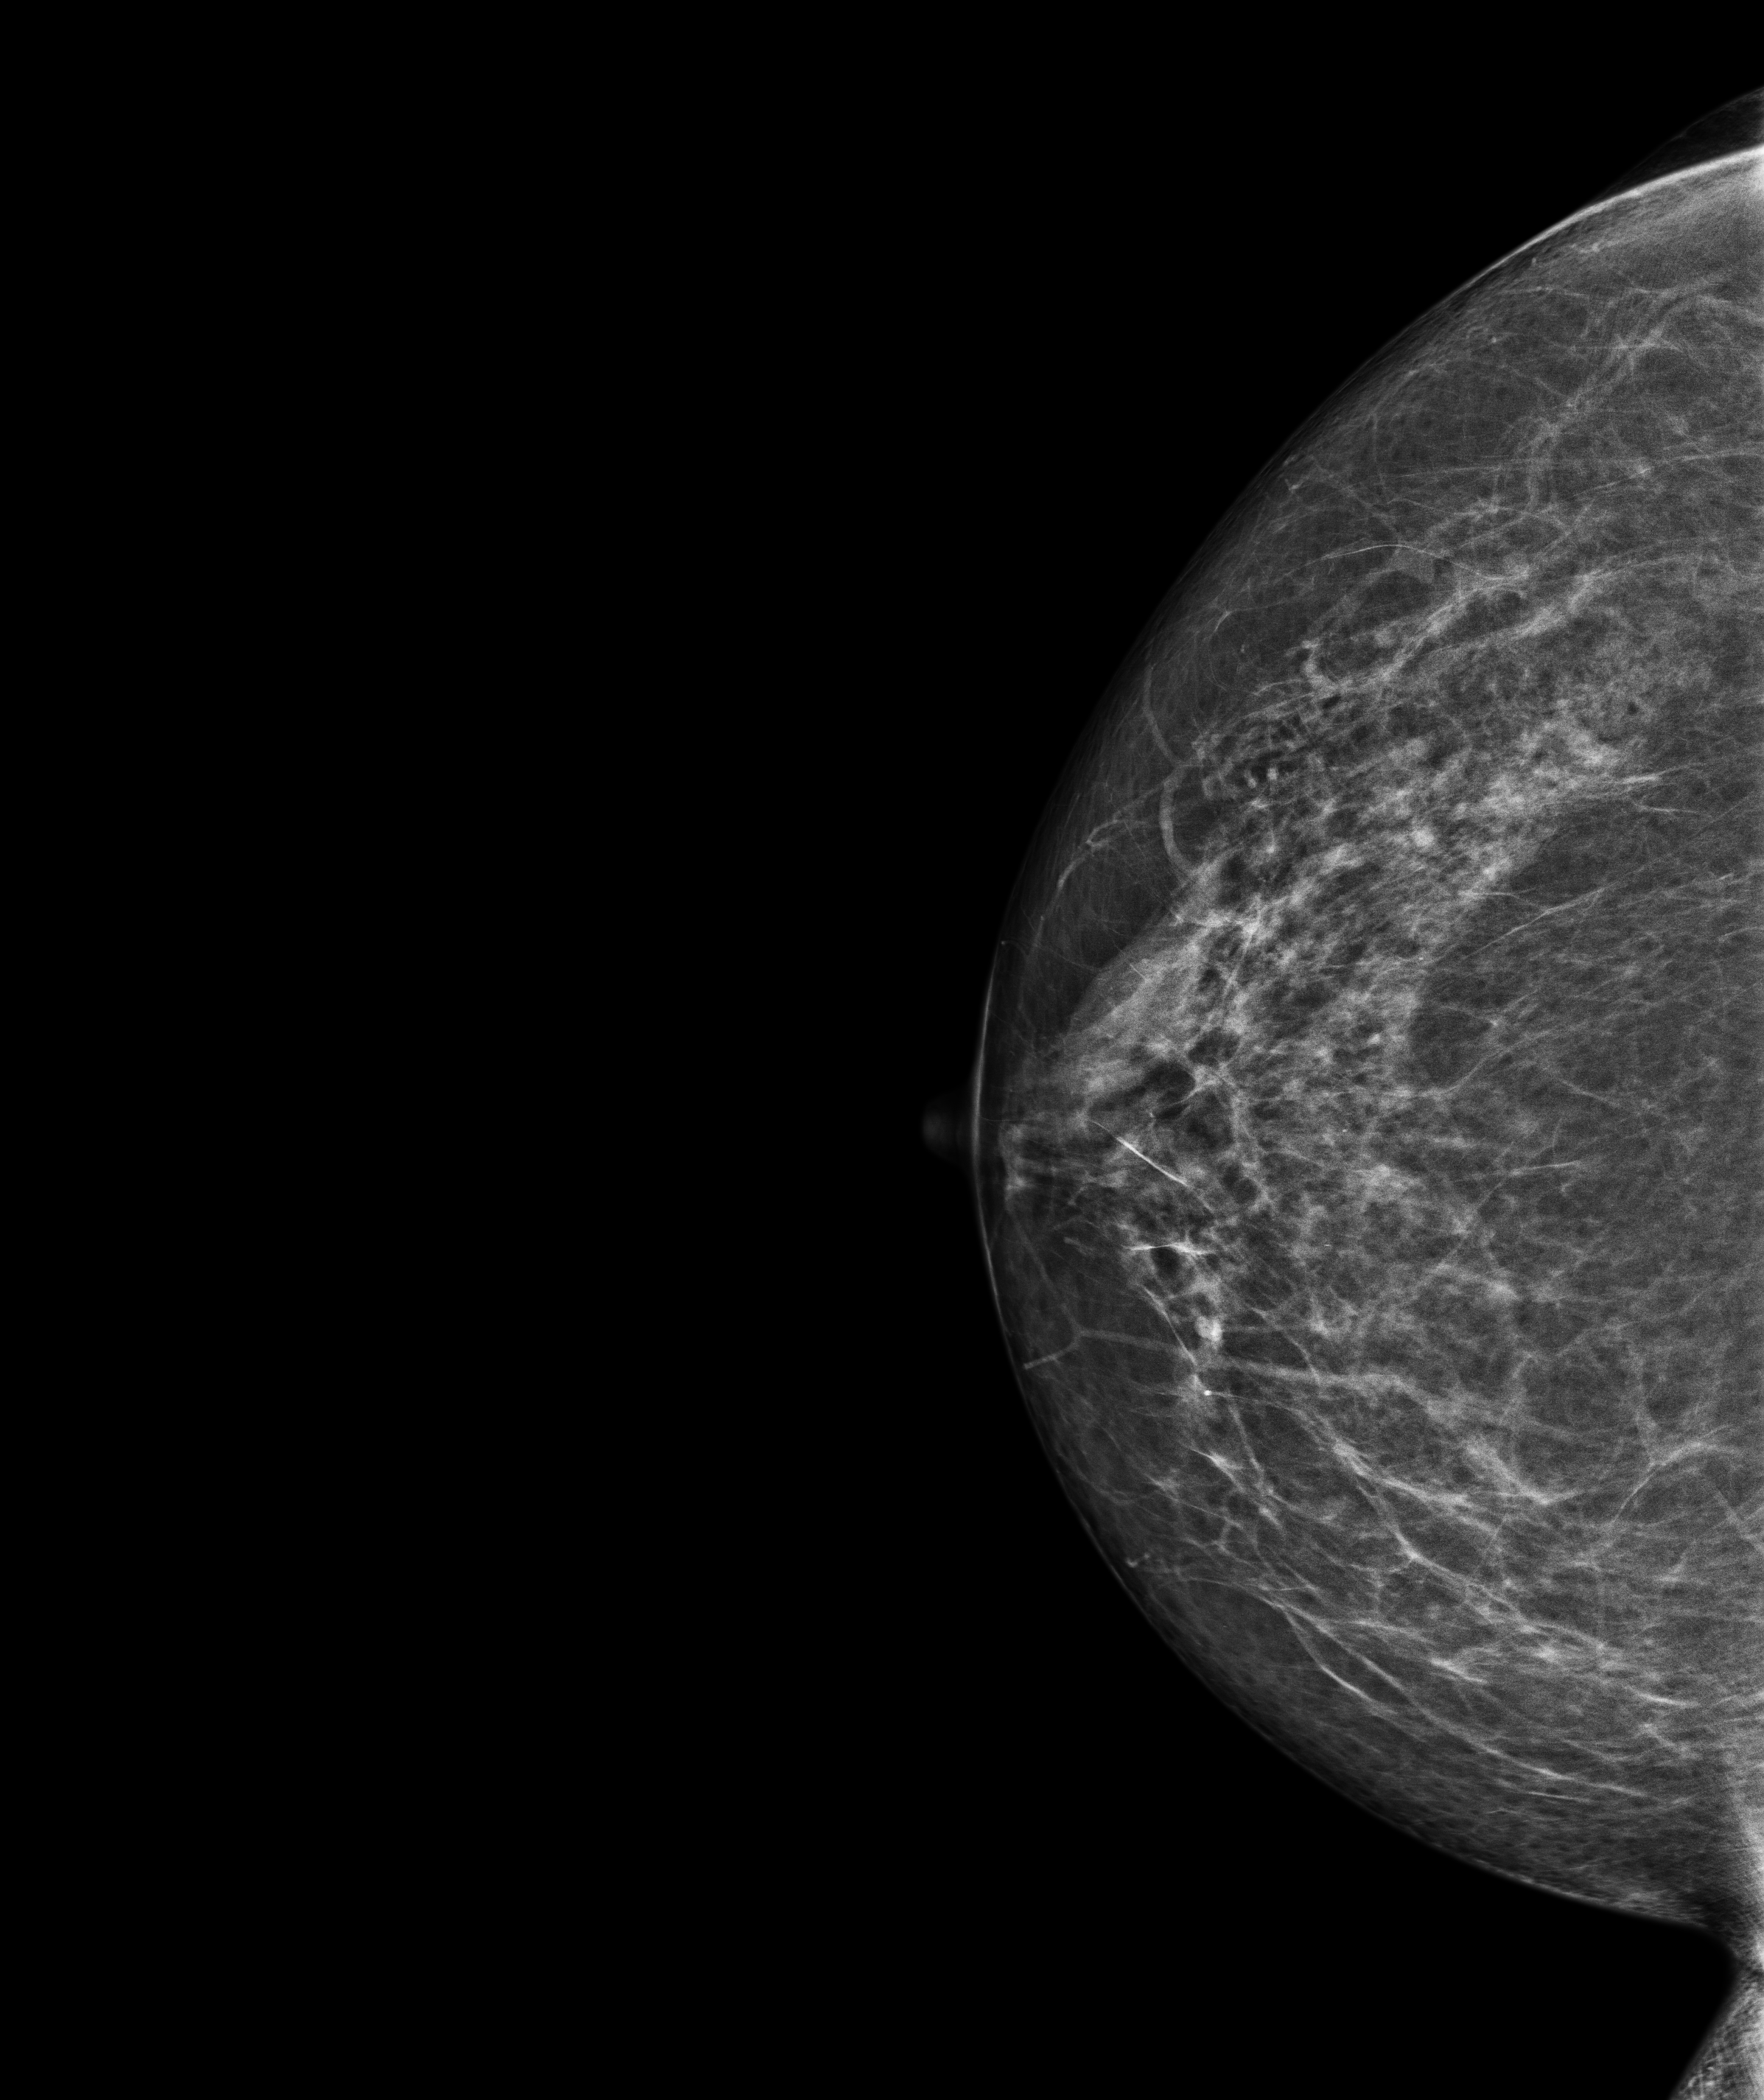
Annual screening mammography examination, compressed breast thickness 76.8 mm, system: Senographe Pristina. Female patient, age 54 years.
Image type: full-field digital mammogram. Breast: right. Projection: craniocaudal (CC) view.